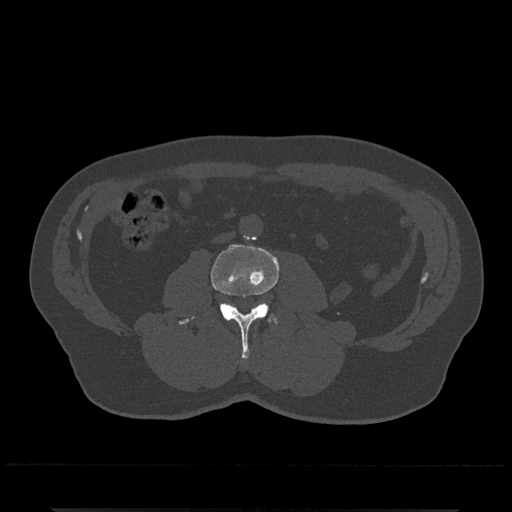
CT including the spine, one axial slice; slice 214 of 797 in the series (ordered by position); reconstruction kernel Br40s/3; 120 kVp; bone window (W 1800 / L 400 HU); 0.5 mm slice thickness; 512 × 512 image matrix. Patient: male, 67 years. Case-level facts recorded for this patient, not image findings: primary cancer: prostate.
Structures marked on this image (semi-automatically segmented with operator editing):
- L3 vertebra: bounding box (x1, y1, x2, y2) in pixels: (179, 244, 280, 359)
- L4 vertebra: (273, 316, 278, 323)